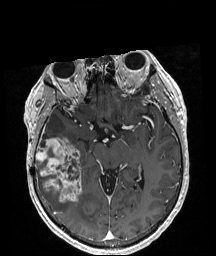
Brain MRI from a brain-tumour surgery series, one axial slice; position 116 of 208 along the scan axis; T1-weighted post-contrast; 1 mm slice thickness; 216 × 256 image matrix. Case-level facts recorded for this patient, not image findings: histopathology: Astrocytoma; WHO grade: 4; IDH mutation: yes; tumour location: Right Temporal.
Structures marked on this image (expert manual segmentation):
- tumour: bounding box <36,137,82,201> (left, top, right, bottom; pixels)